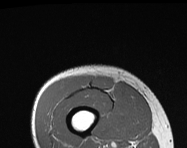
MRI of an extremity soft-tissue mass, one axial slice. Position 30 of 114 along the scan axis. MR volume resampled by the dataset authors to the PET/CT grid (not the native acquisition matrix). 3.27 mm slice thickness. 187 × 148 image matrix, field of view 183 × 145 mm. Male patient. Case-level facts recorded for this patient, not image findings: histological type: pleiomorphic leiomyosarcoma; grade: intermediate; site of the primary tumour: right thigh.
Outlined on this slice (expert contour drawn on MRI and transferred to this co-registered scan by the dataset authors):
- gross tumour volume including surrounding oedema: bounding box [x1, y1, x2, y2] px = [91, 77, 113, 91]